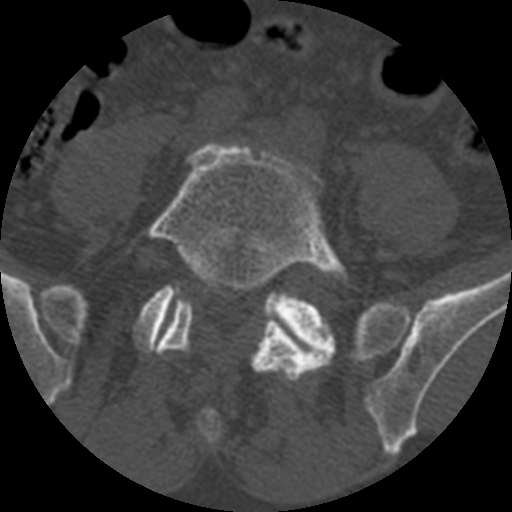
CT including the spine, one axial slice. Position 252 of 399 along the scan axis. Bone window (W 1800 / L 400 HU). 512 × 512 image matrix. Patient age 71 years. Case-level facts recorded for this patient, not image findings: primary cancer: prostate.
Outlined on this slice (semi-automatically segmented with operator editing):
- L5 vertebra: bounding box (x1, y1, x2, y2) in pixels: (144, 143, 349, 383)